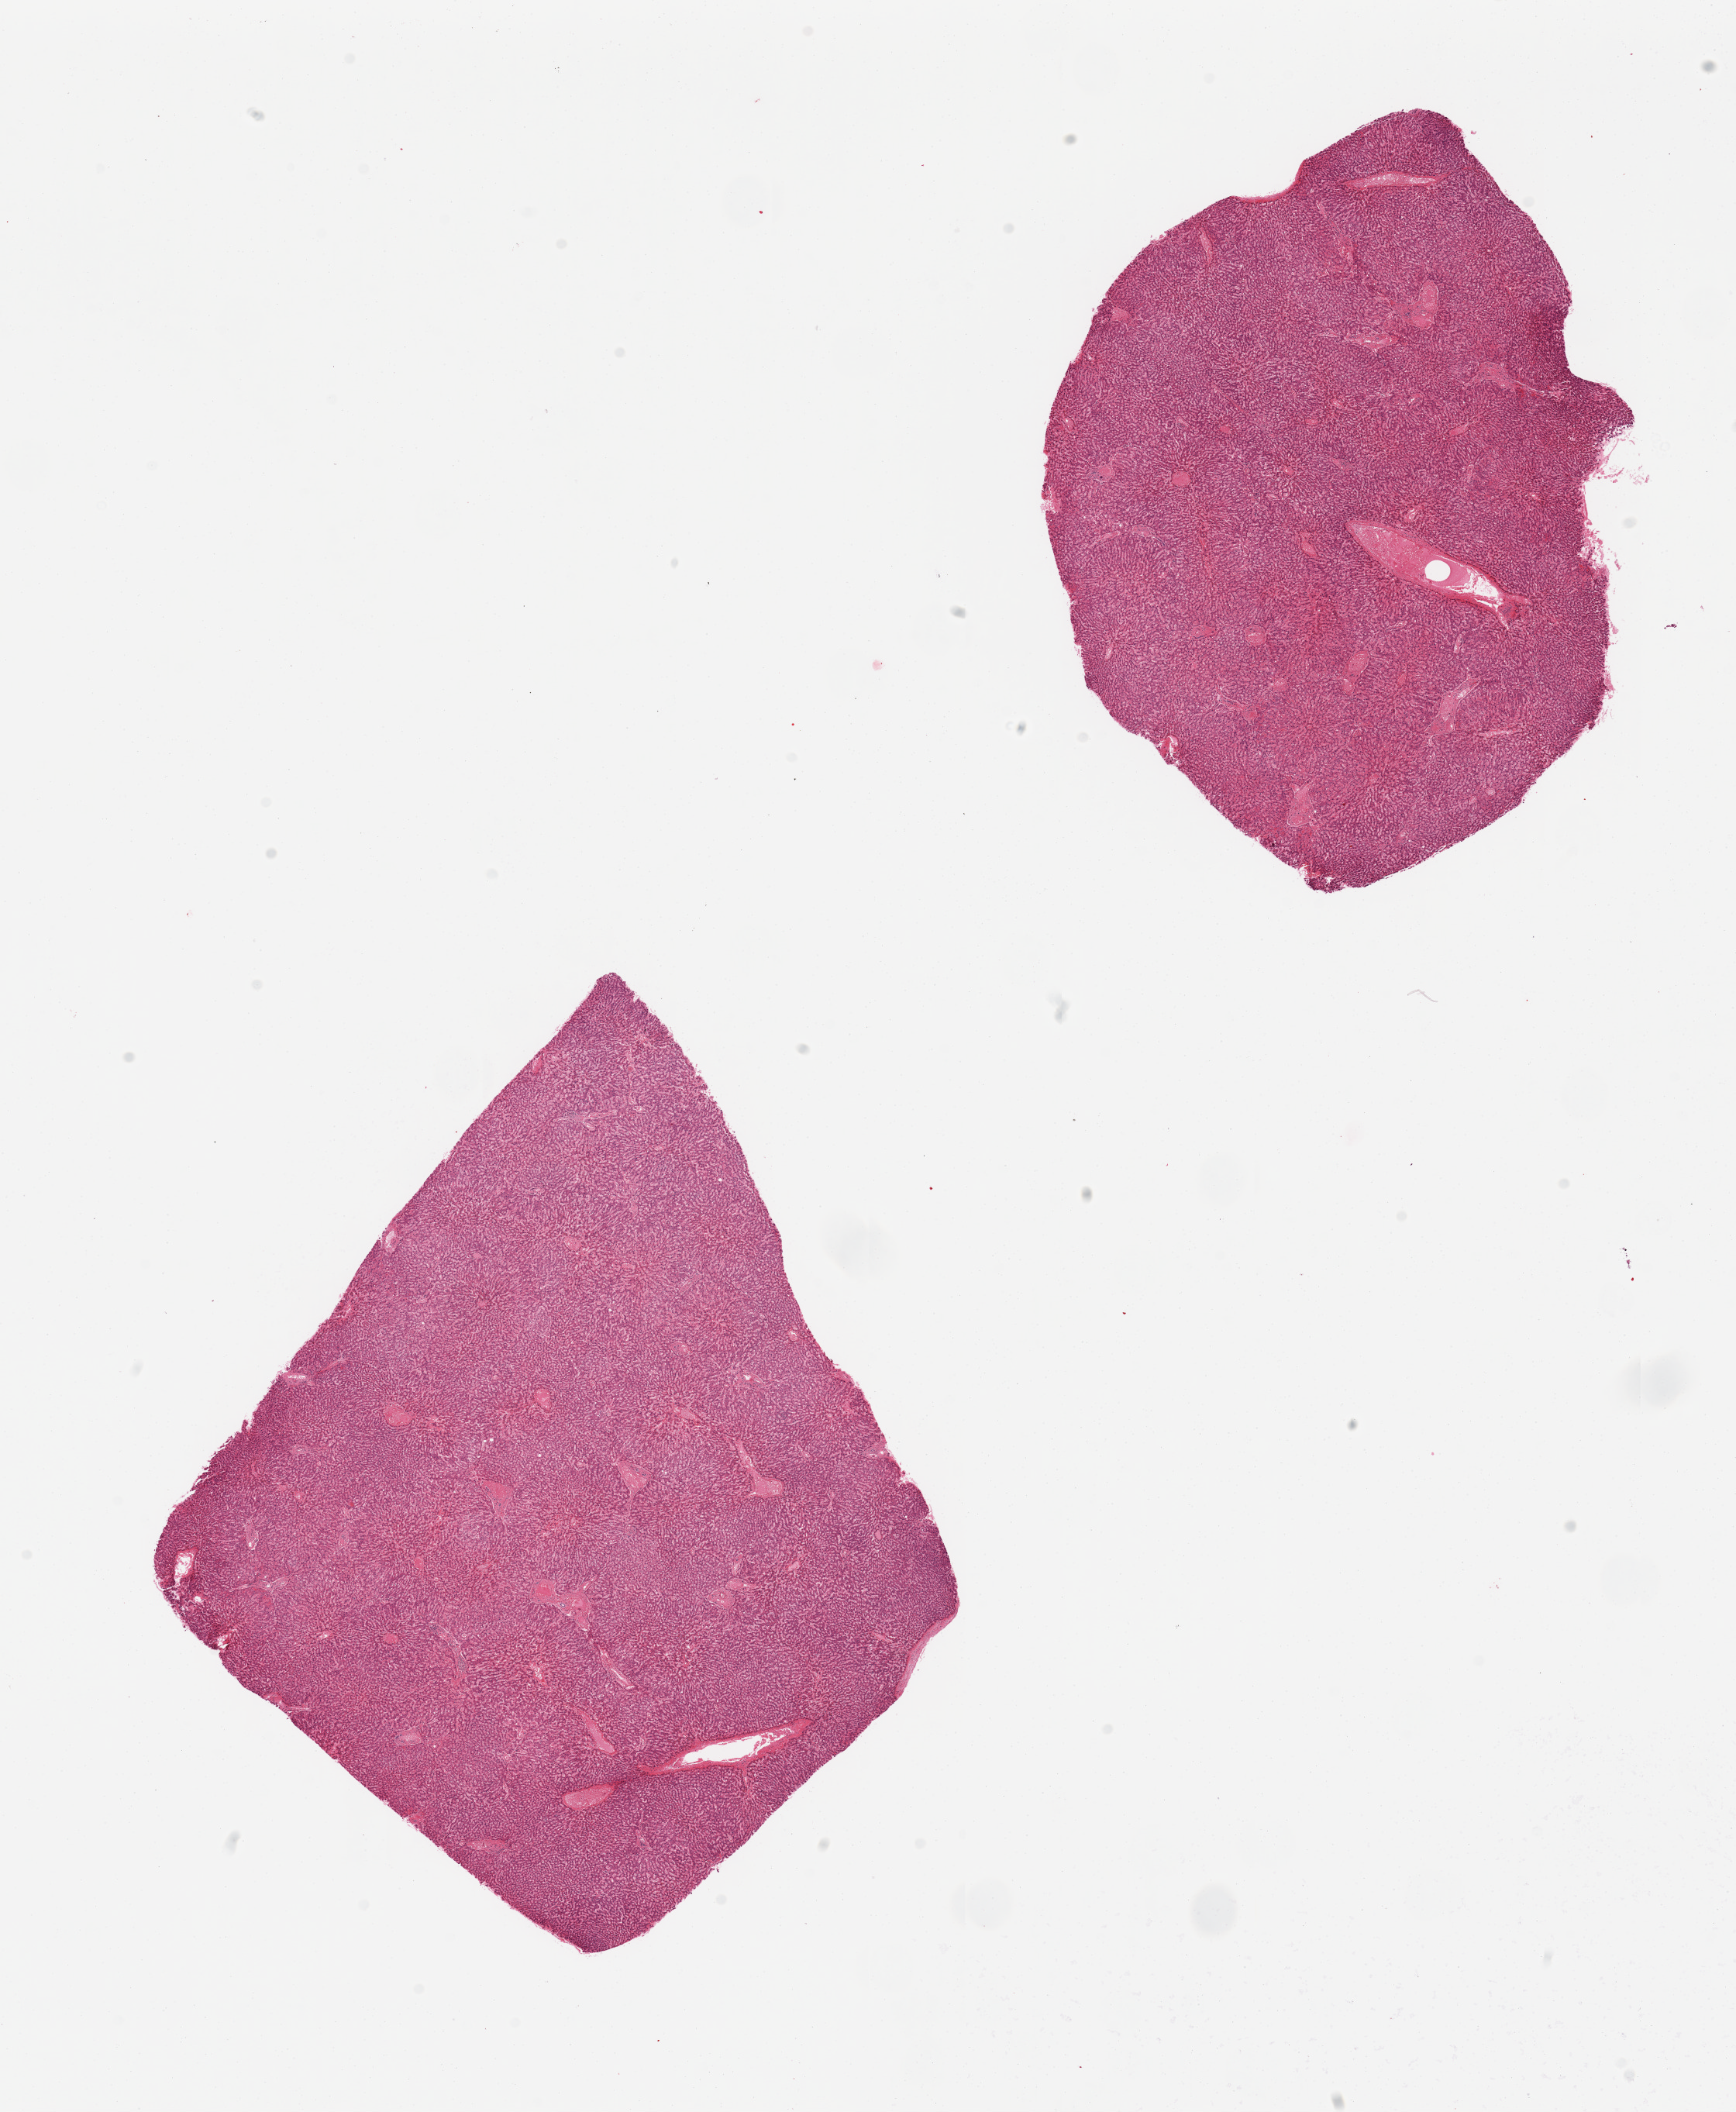
Digitized haematoxylin and eosin-stained section — shown as a low-resolution overview of the whole scanned area (about 17.7 x 21.6 mm); PAXgene-fixed, paraffin-embedded tissue; section of liver (target tissue); tissue donor sample. Donor: male.
Reviewer comment on this tissue sample: 2 pieces, congestion.